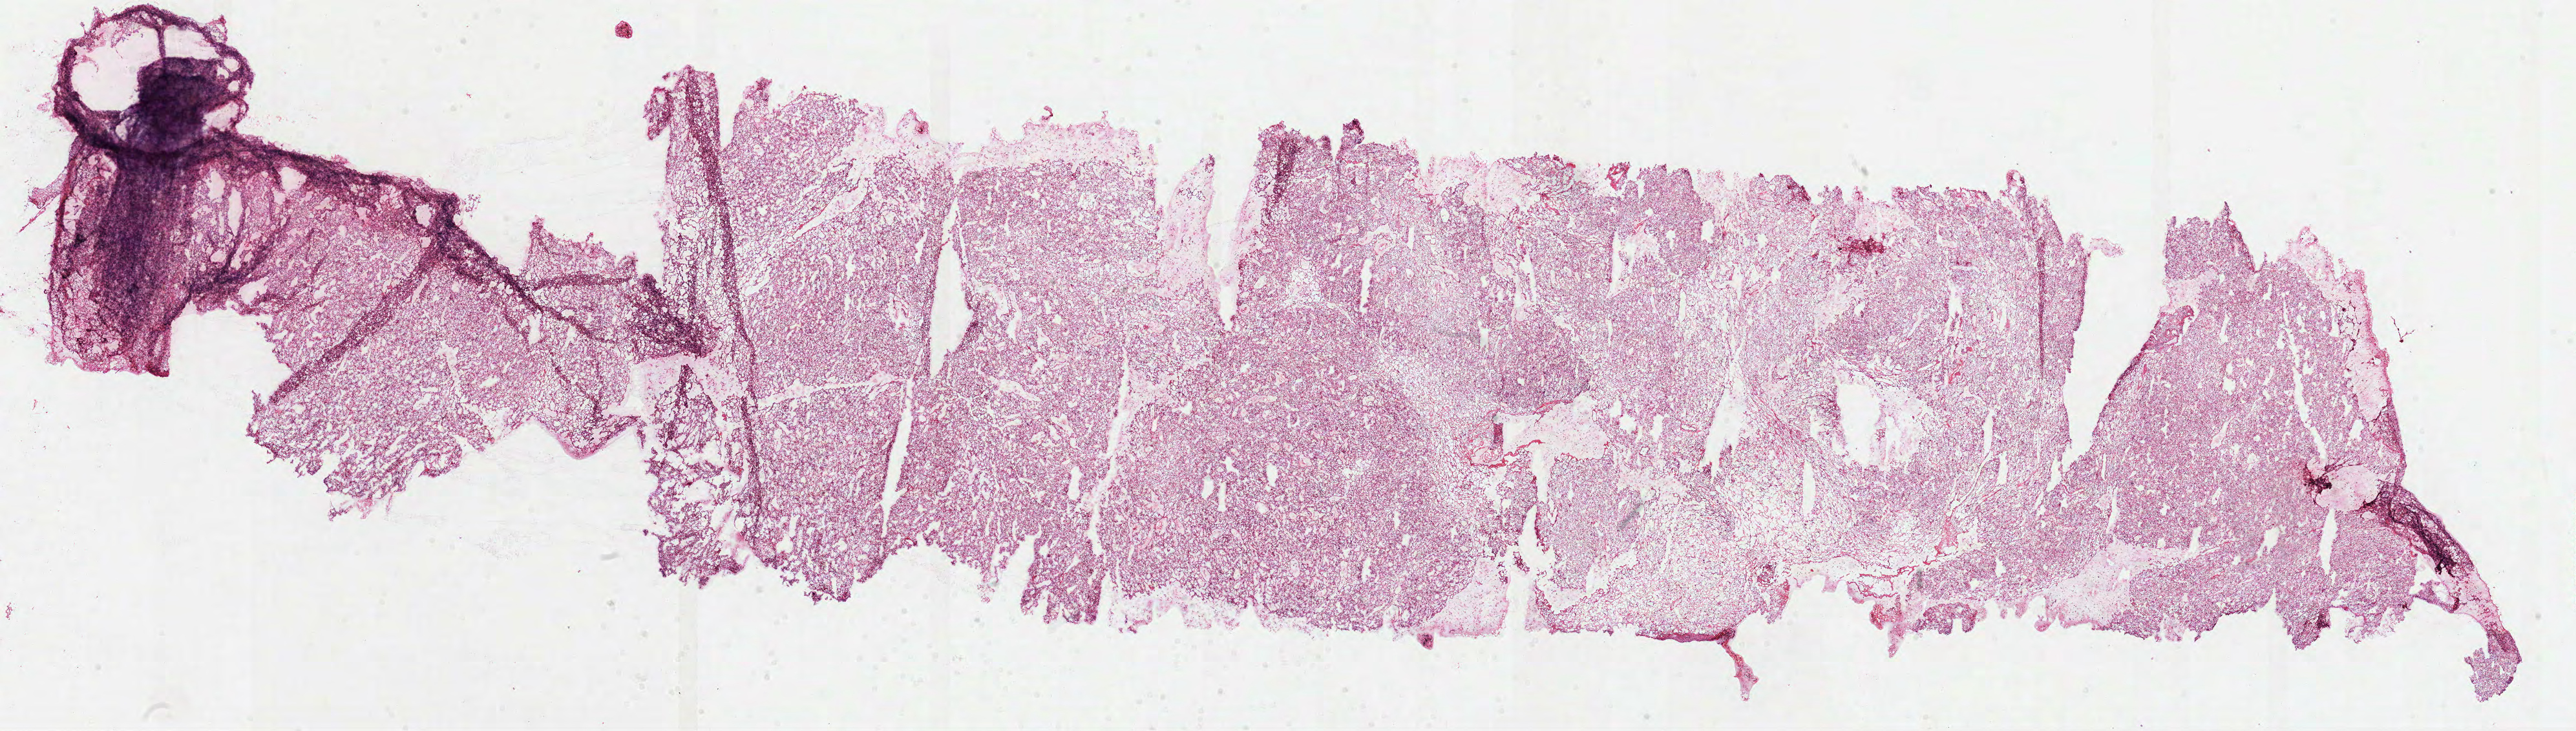
H&E whole-slide image, shown as a low-resolution overview of the whole scanned area (about 32.1 x 9.1 mm, from a 40x scan). Frozen section from the top of the tissue portion. Sample: primary tumour, kidney. Patient: female, age at initial diagnosis 63 years. Histologic grade: G3 (poorly differentiated). Pathologist review of this section (percent, as recorded): tumour cells 90%, tumour nuclei 80%, normal cells 0%, stromal cells 10%, necrosis 0%.
AJCC pathologic stage: II. Histologic diagnosis: Clear cell adenocarcinoma, NOS.